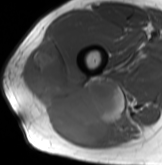
MRI of an extremity soft-tissue mass, one axial slice; slice 58 of 61 in the series (ordered by position); MR volume resampled by the dataset authors to the PET/CT grid (not the native acquisition matrix); 3.27 mm slice thickness; 162 × 165 image matrix, field of view 158 × 161 mm. Male patient. Case-level facts recorded for this patient, not image findings: histological type: poorly differentiated synovial sarcoma; grade: high; site of the primary tumour: right buttock.
Outlined on this slice (expert contour drawn on MRI and transferred to this co-registered scan by the dataset authors):
- gross tumour volume including surrounding oedema: bounding box <20,38,138,146> (left, top, right, bottom; pixels)
- gross tumour volume (mass): <22,38,126,146>